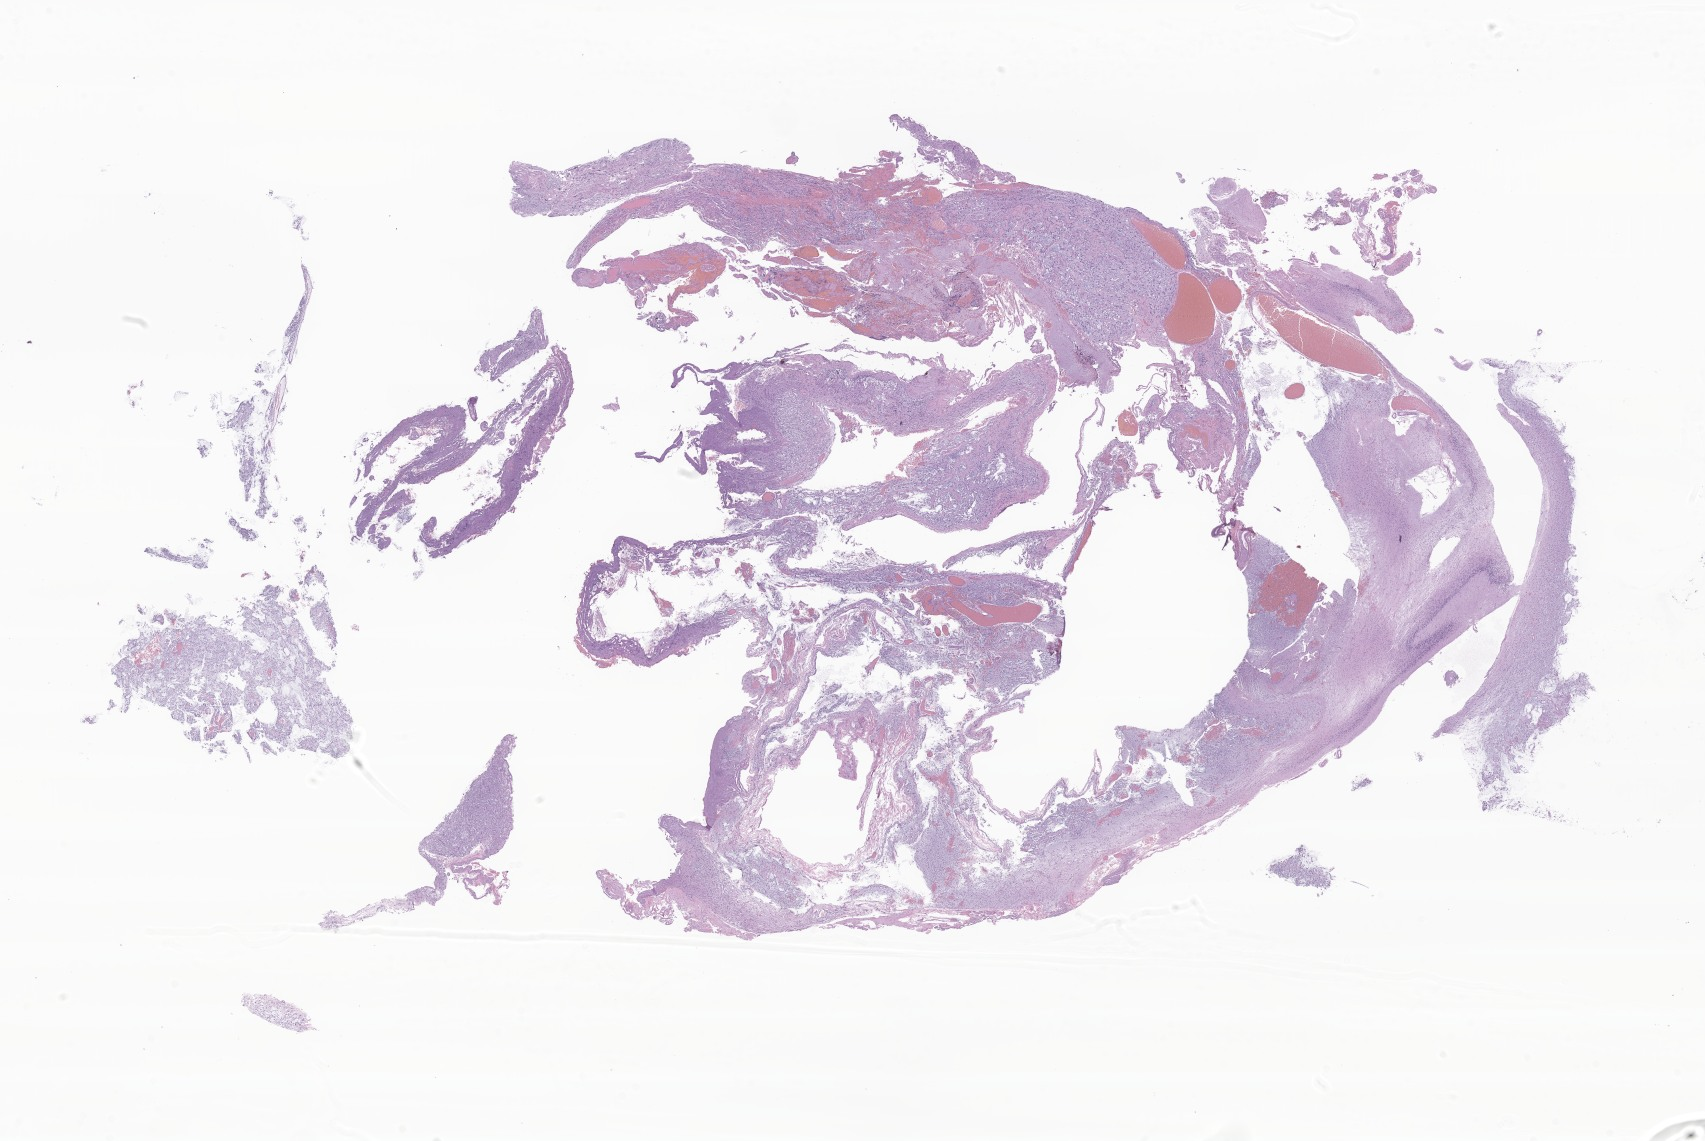
H&E whole-slide image of tumor tissue from the brain, shown as a low-resolution overview of the whole scanned area (about 28.8 x 19.2 mm); formalin-fixed paraffin-embedded section. Patient female; age 156 months (13 years).
- recorded diagnosis: Neoplasm, malignant